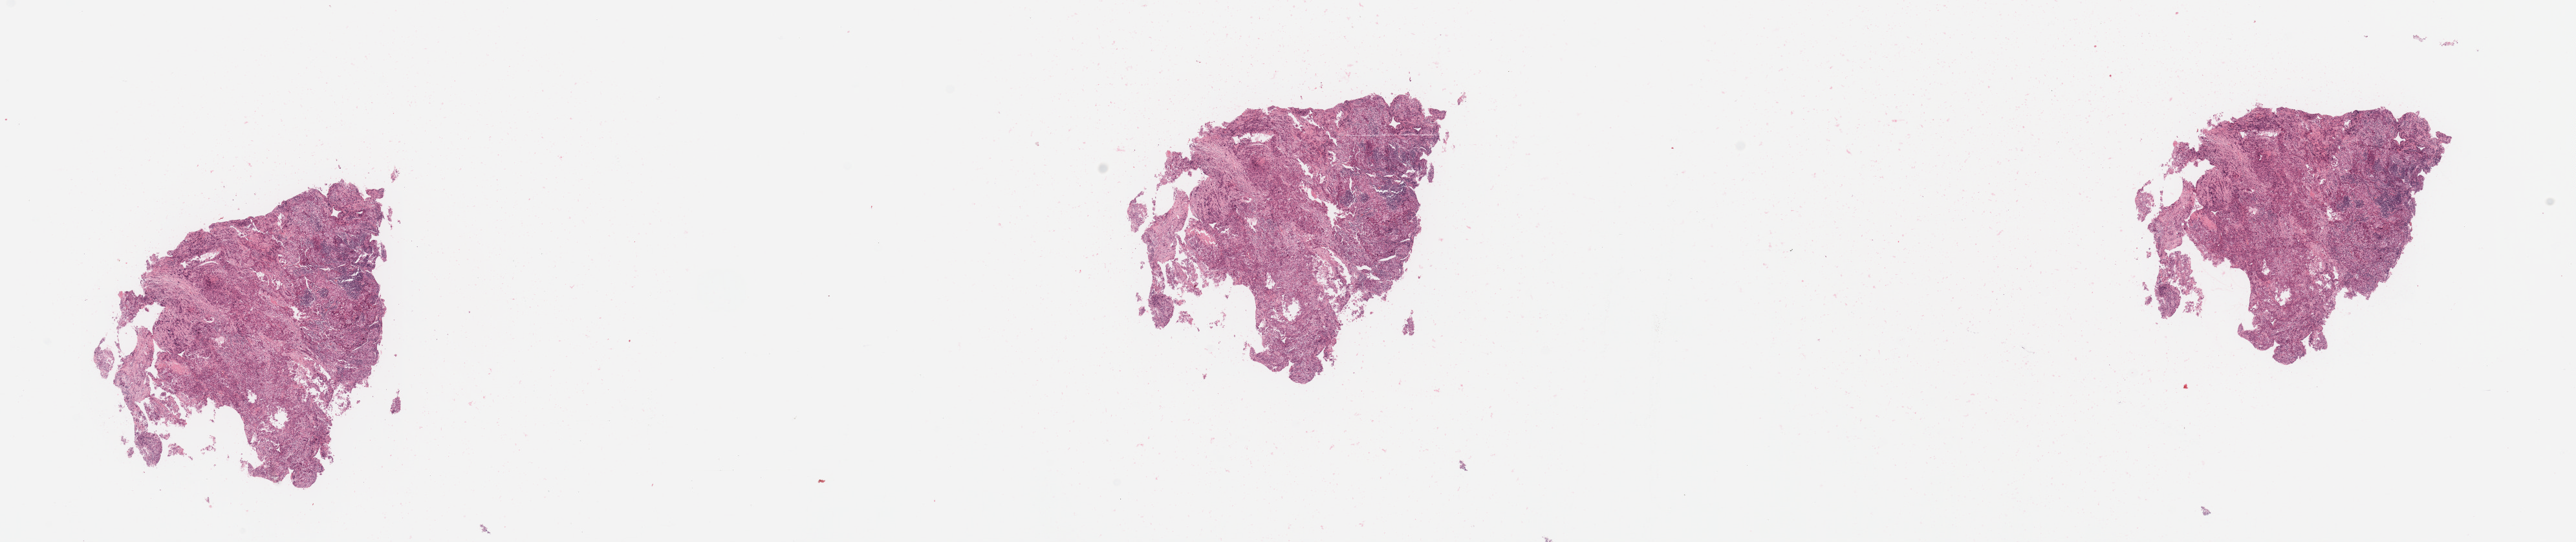
Whole-slide histology image, H&E — shown as a low-resolution overview of the whole scanned area (about 31.5 x 6.6 mm); lung, tumour tissue. Patient: female, age 47 years. Histologic grade: G3 (poorly differentiated).
AJCC pathologic stage: IB. Histologic diagnosis: Adenocarcinoma, NOS. Primary tumour site (as recorded): right middle lobe.